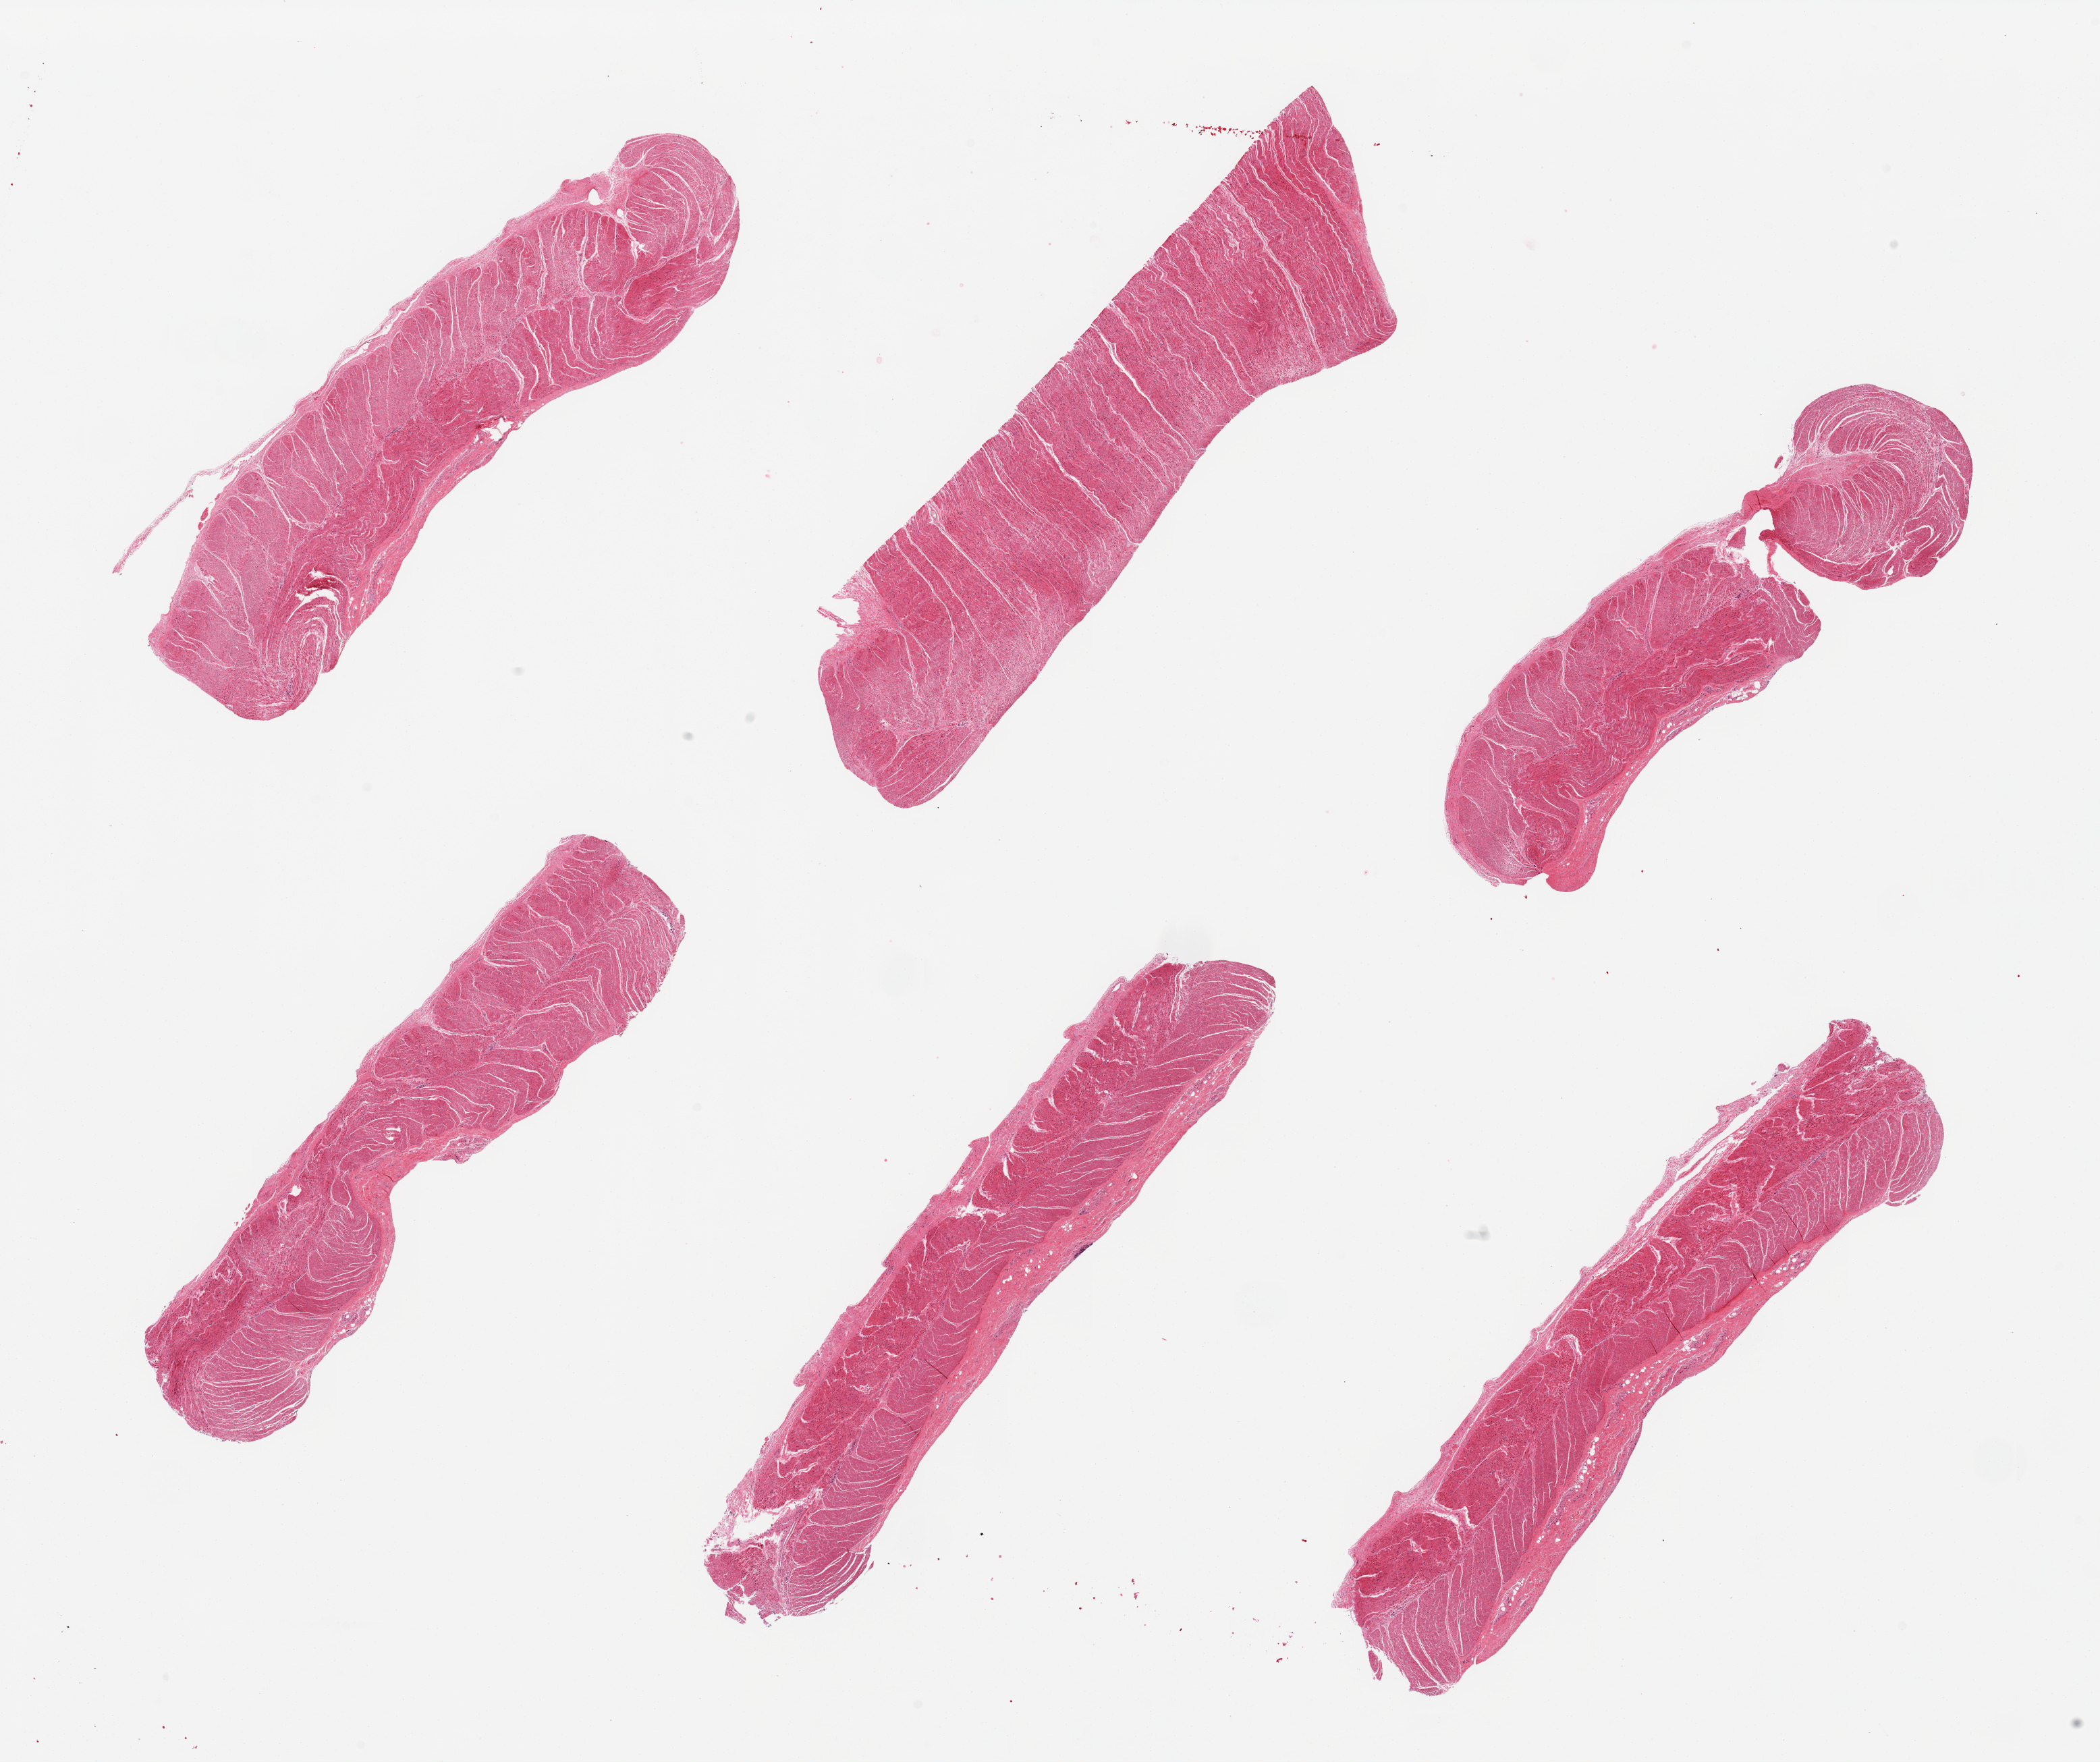
Whole-slide image, haematoxylin and eosin stain — shown as a low-resolution overview of the whole scanned area (about 24.6 x 20.6 mm, slide scanned at 20x), PAXgene-fixed paraffin-embedded (PFPE) section, target tissue: sigmoid colon, tissue donor sample.
Reviewer comment on this tissue sample: 6 pieces, all muscularis, good specimens.